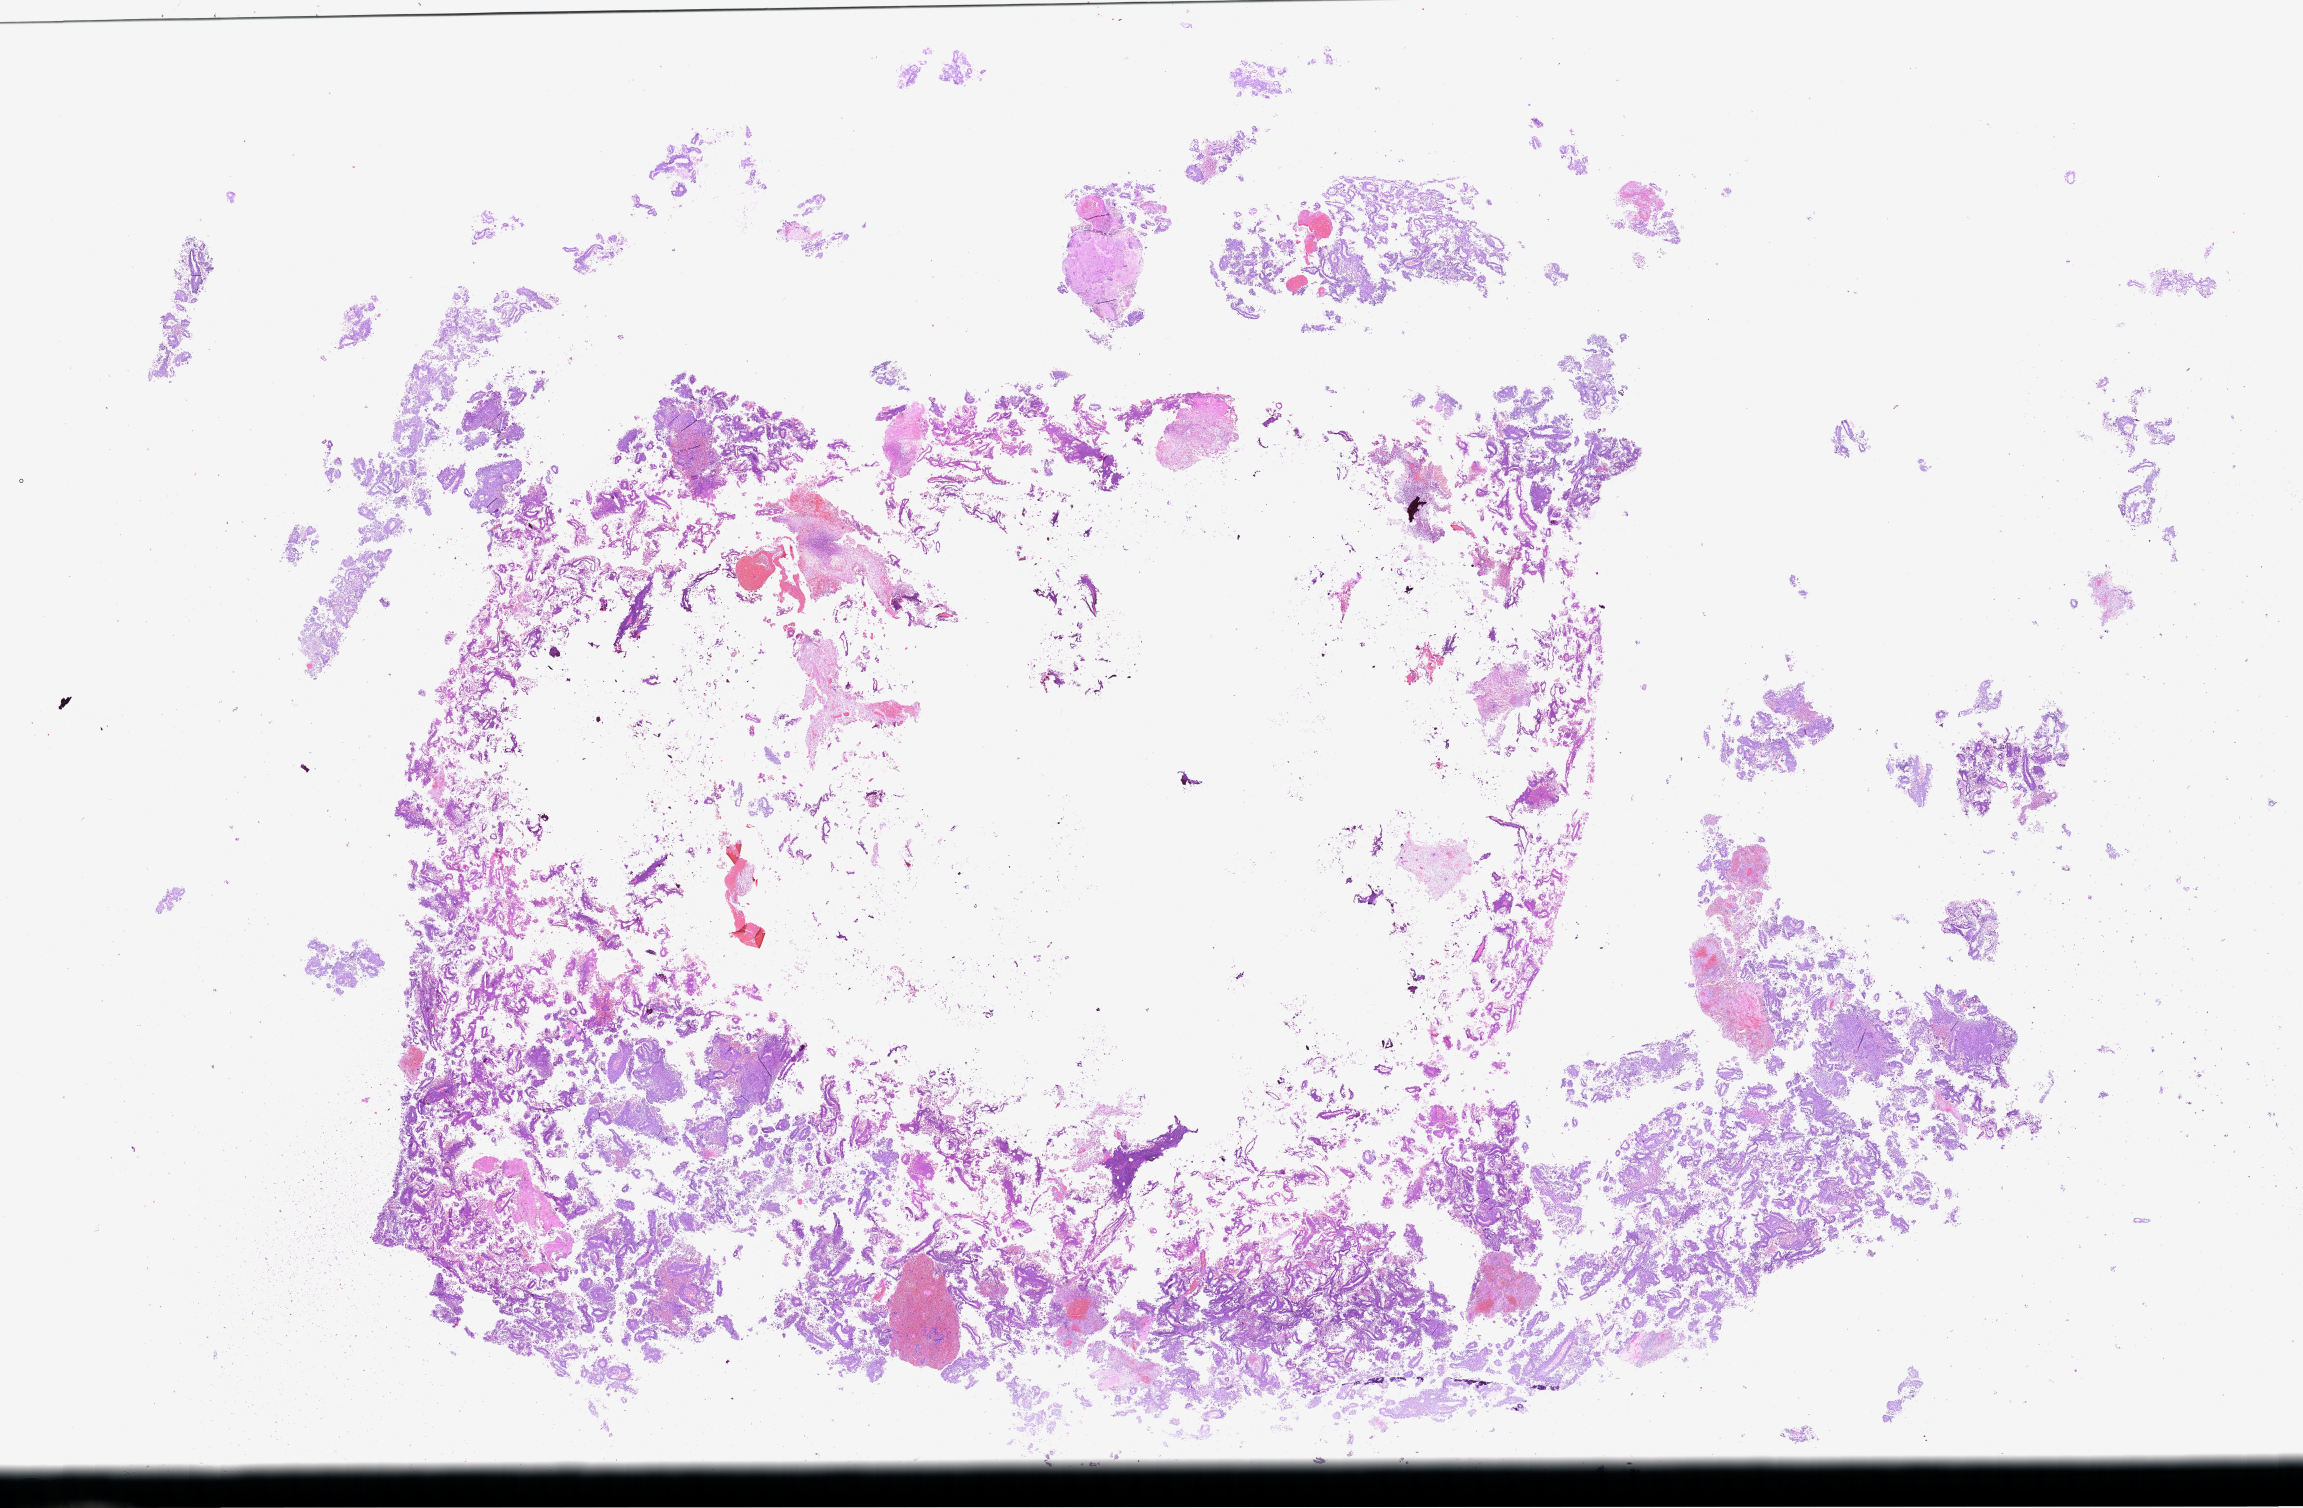
Digitized haematoxylin and eosin-stained section — whole scanned area (about 37.2 x 24.4 mm) shown as a low-resolution overview; FFPE section. Patient sex: female.
* this section: metastasis (sampled organ not recorded)
* primary diagnosis of the patient: Melanoma